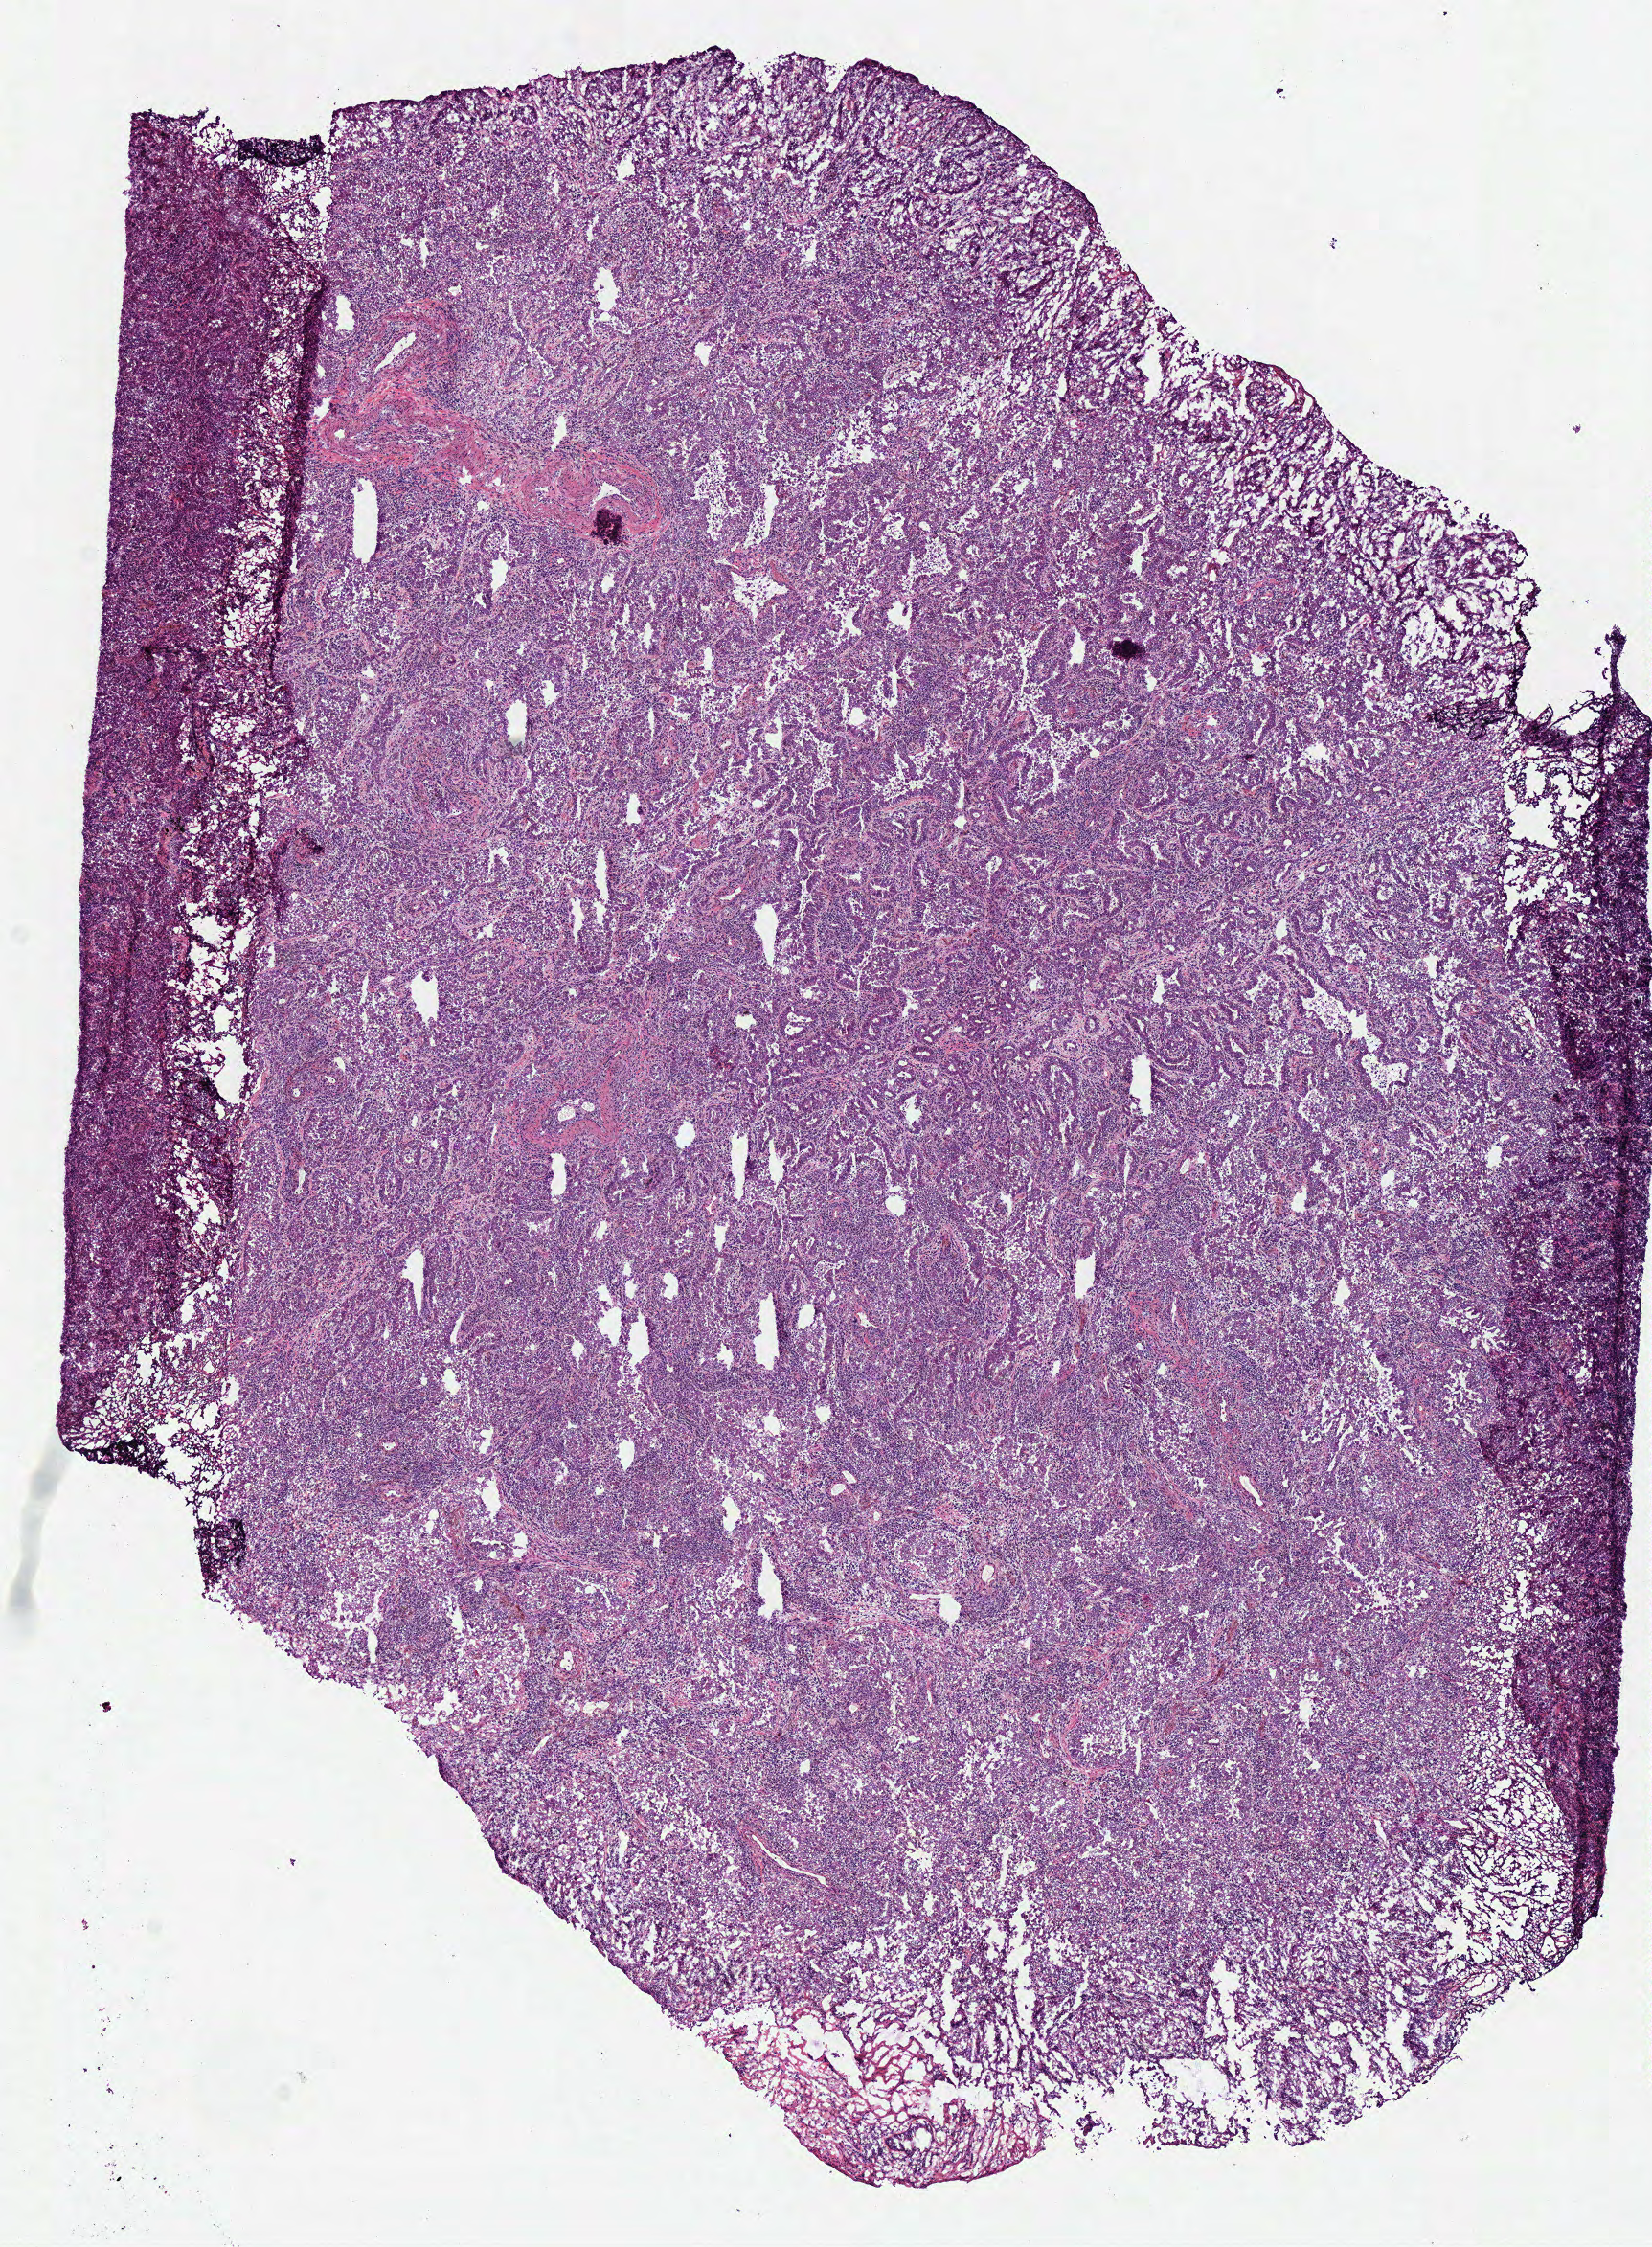
Hematoxylin and eosin (H&E) stained whole-slide image — shown as a low-resolution overview of the whole scanned area (about 6.8 x 9.2 mm, acquisition: 40x scan), frozen section from the top of the tissue portion, lung, primary tumour sample. Female, age 73 years at initial diagnosis. Composition of this section per pathologist review: tumour cells 90%, tumour nuclei 80%, normal cells 0%, stromal cells 10%, necrosis 0%.
* pathologic diagnosis: Adenocarcinoma with mixed subtypes (upper lobe, lung)
* laterality: left
* AJCC pathologic stage: IIA (7th edition)